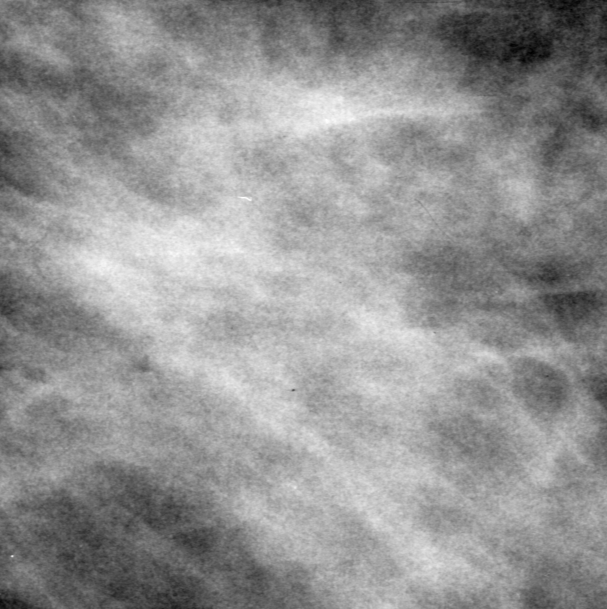
Cropped region of a digitized screen-film mammogram centred on a radiologist-marked abnormality; left breast; MLO view; BI-RADS breast density category 3 (scale 1–4).
- Marked abnormality: mass, shape architectural distortion; BI-RADS assessment category 0 (incomplete: needs additional imaging); subtlety rating 5 on a 1 (subtle) to 5 (obvious) scale; pathology result (as recorded, not read from the image): malignant.